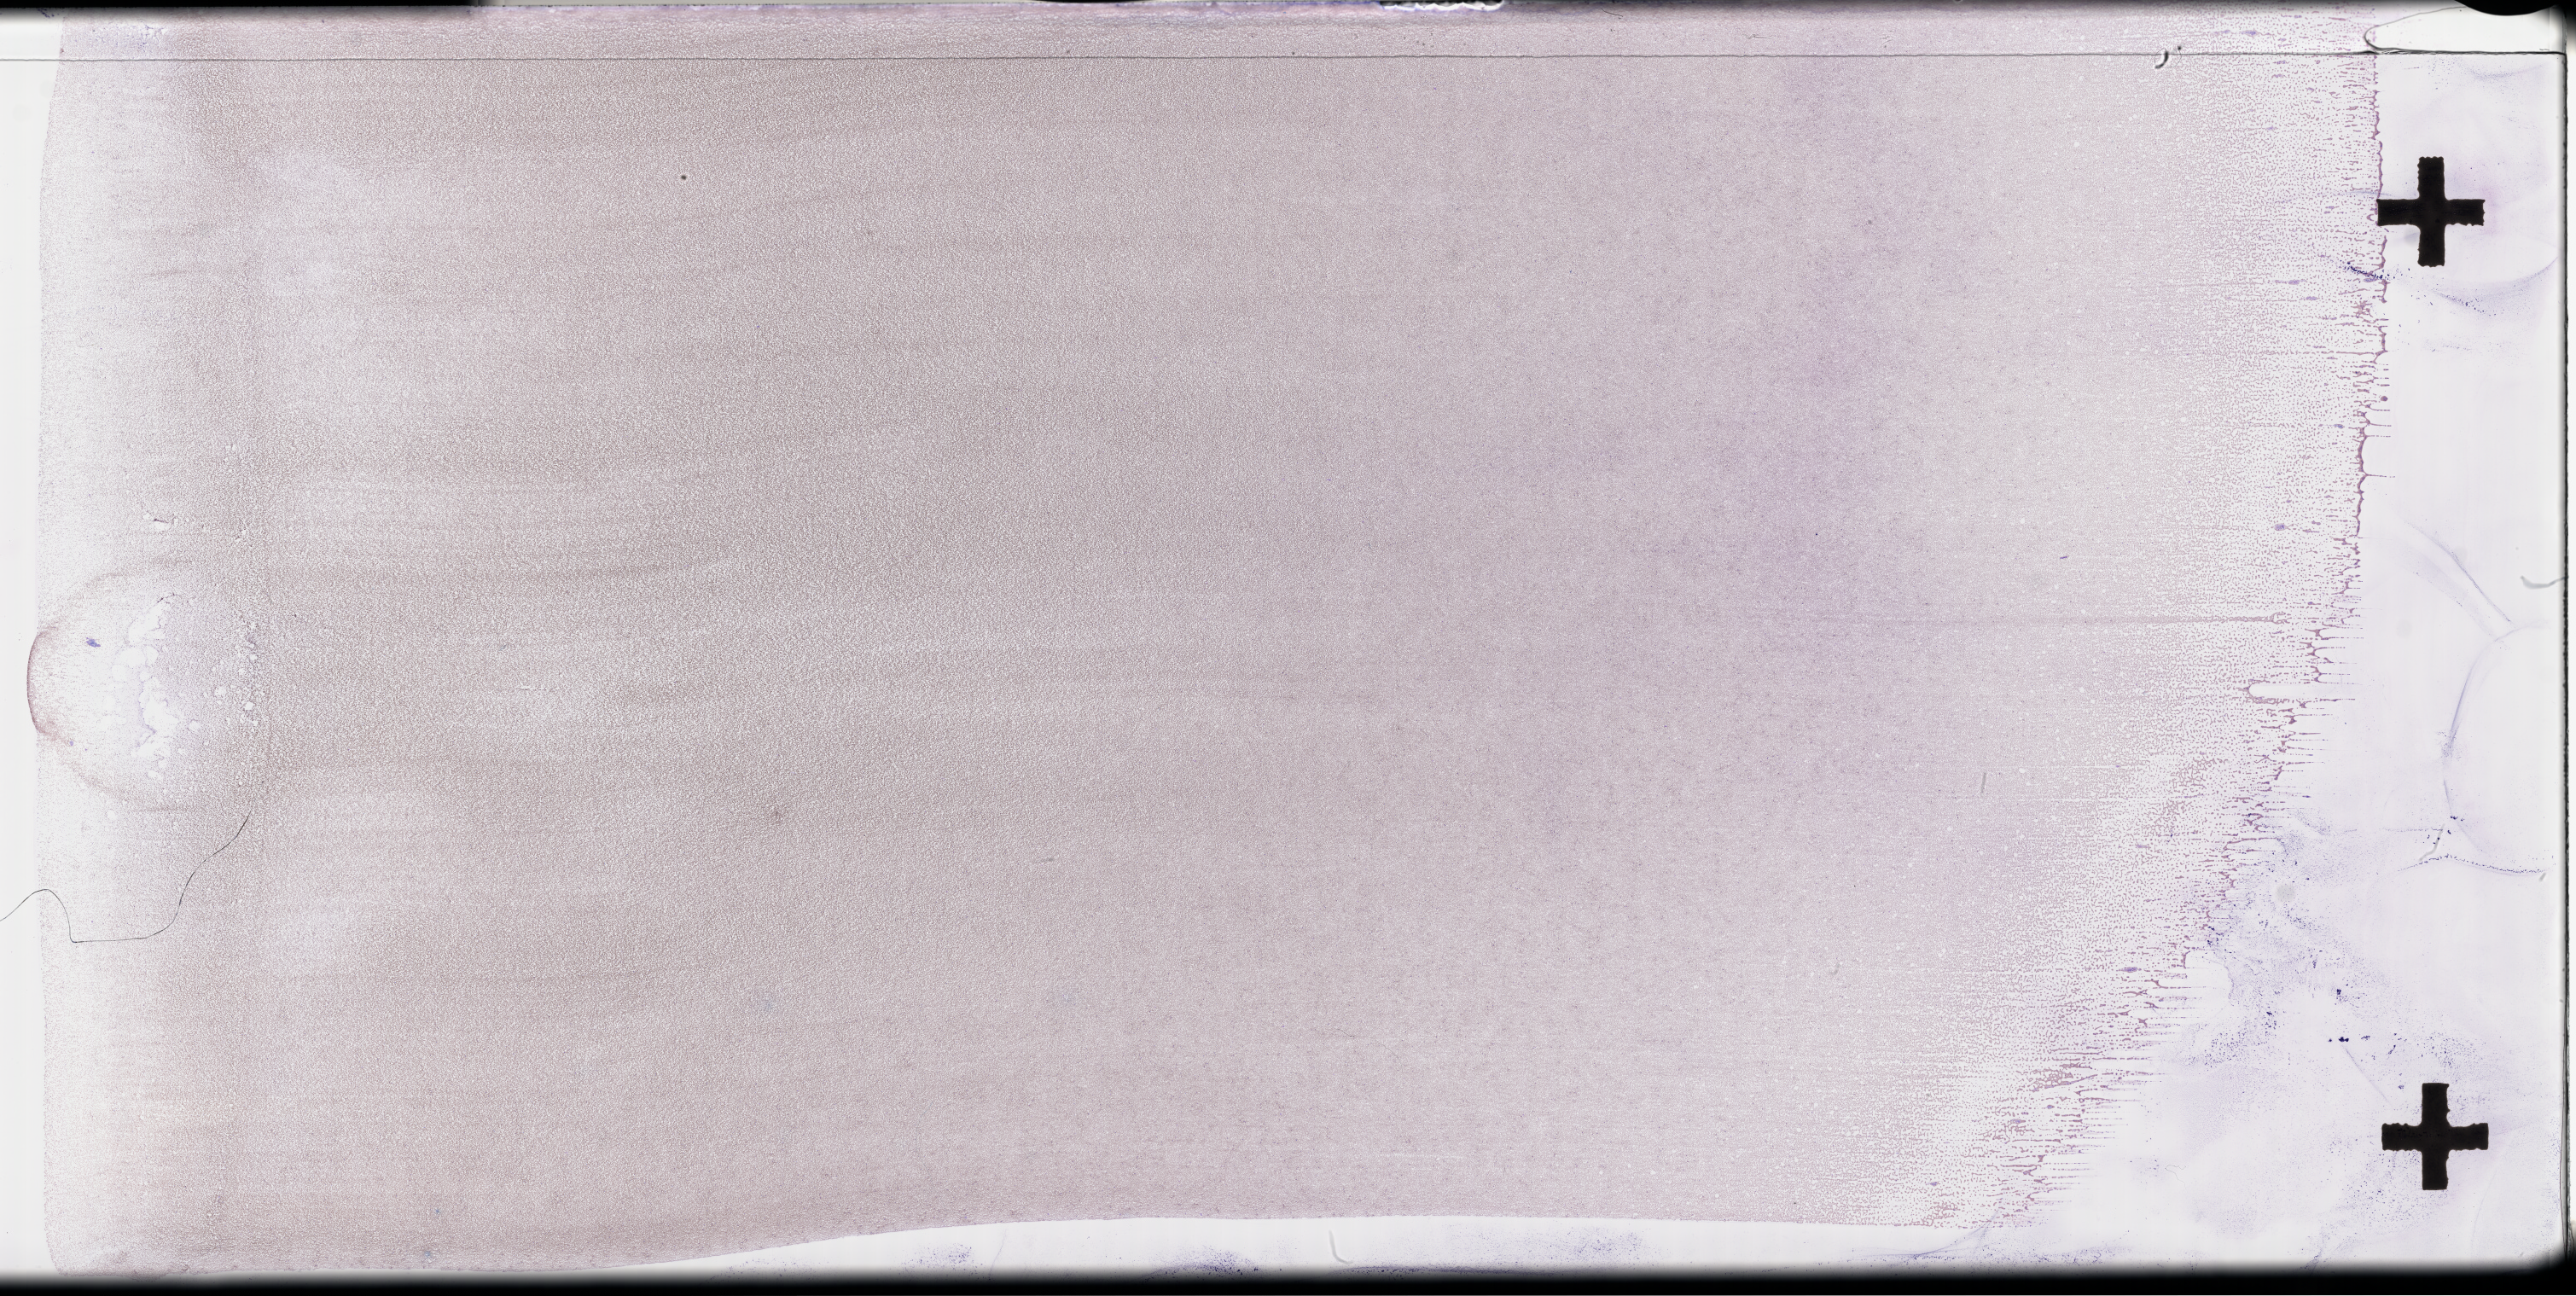
Whole-slide image of a whole blood smear, Wright–Giemsa stain — a low-resolution overview of the entire scanned area, about 48.8 x 24.5 mm. Collected on treatment. Male patient.
From a patient with: Plasma Cell Myeloma.